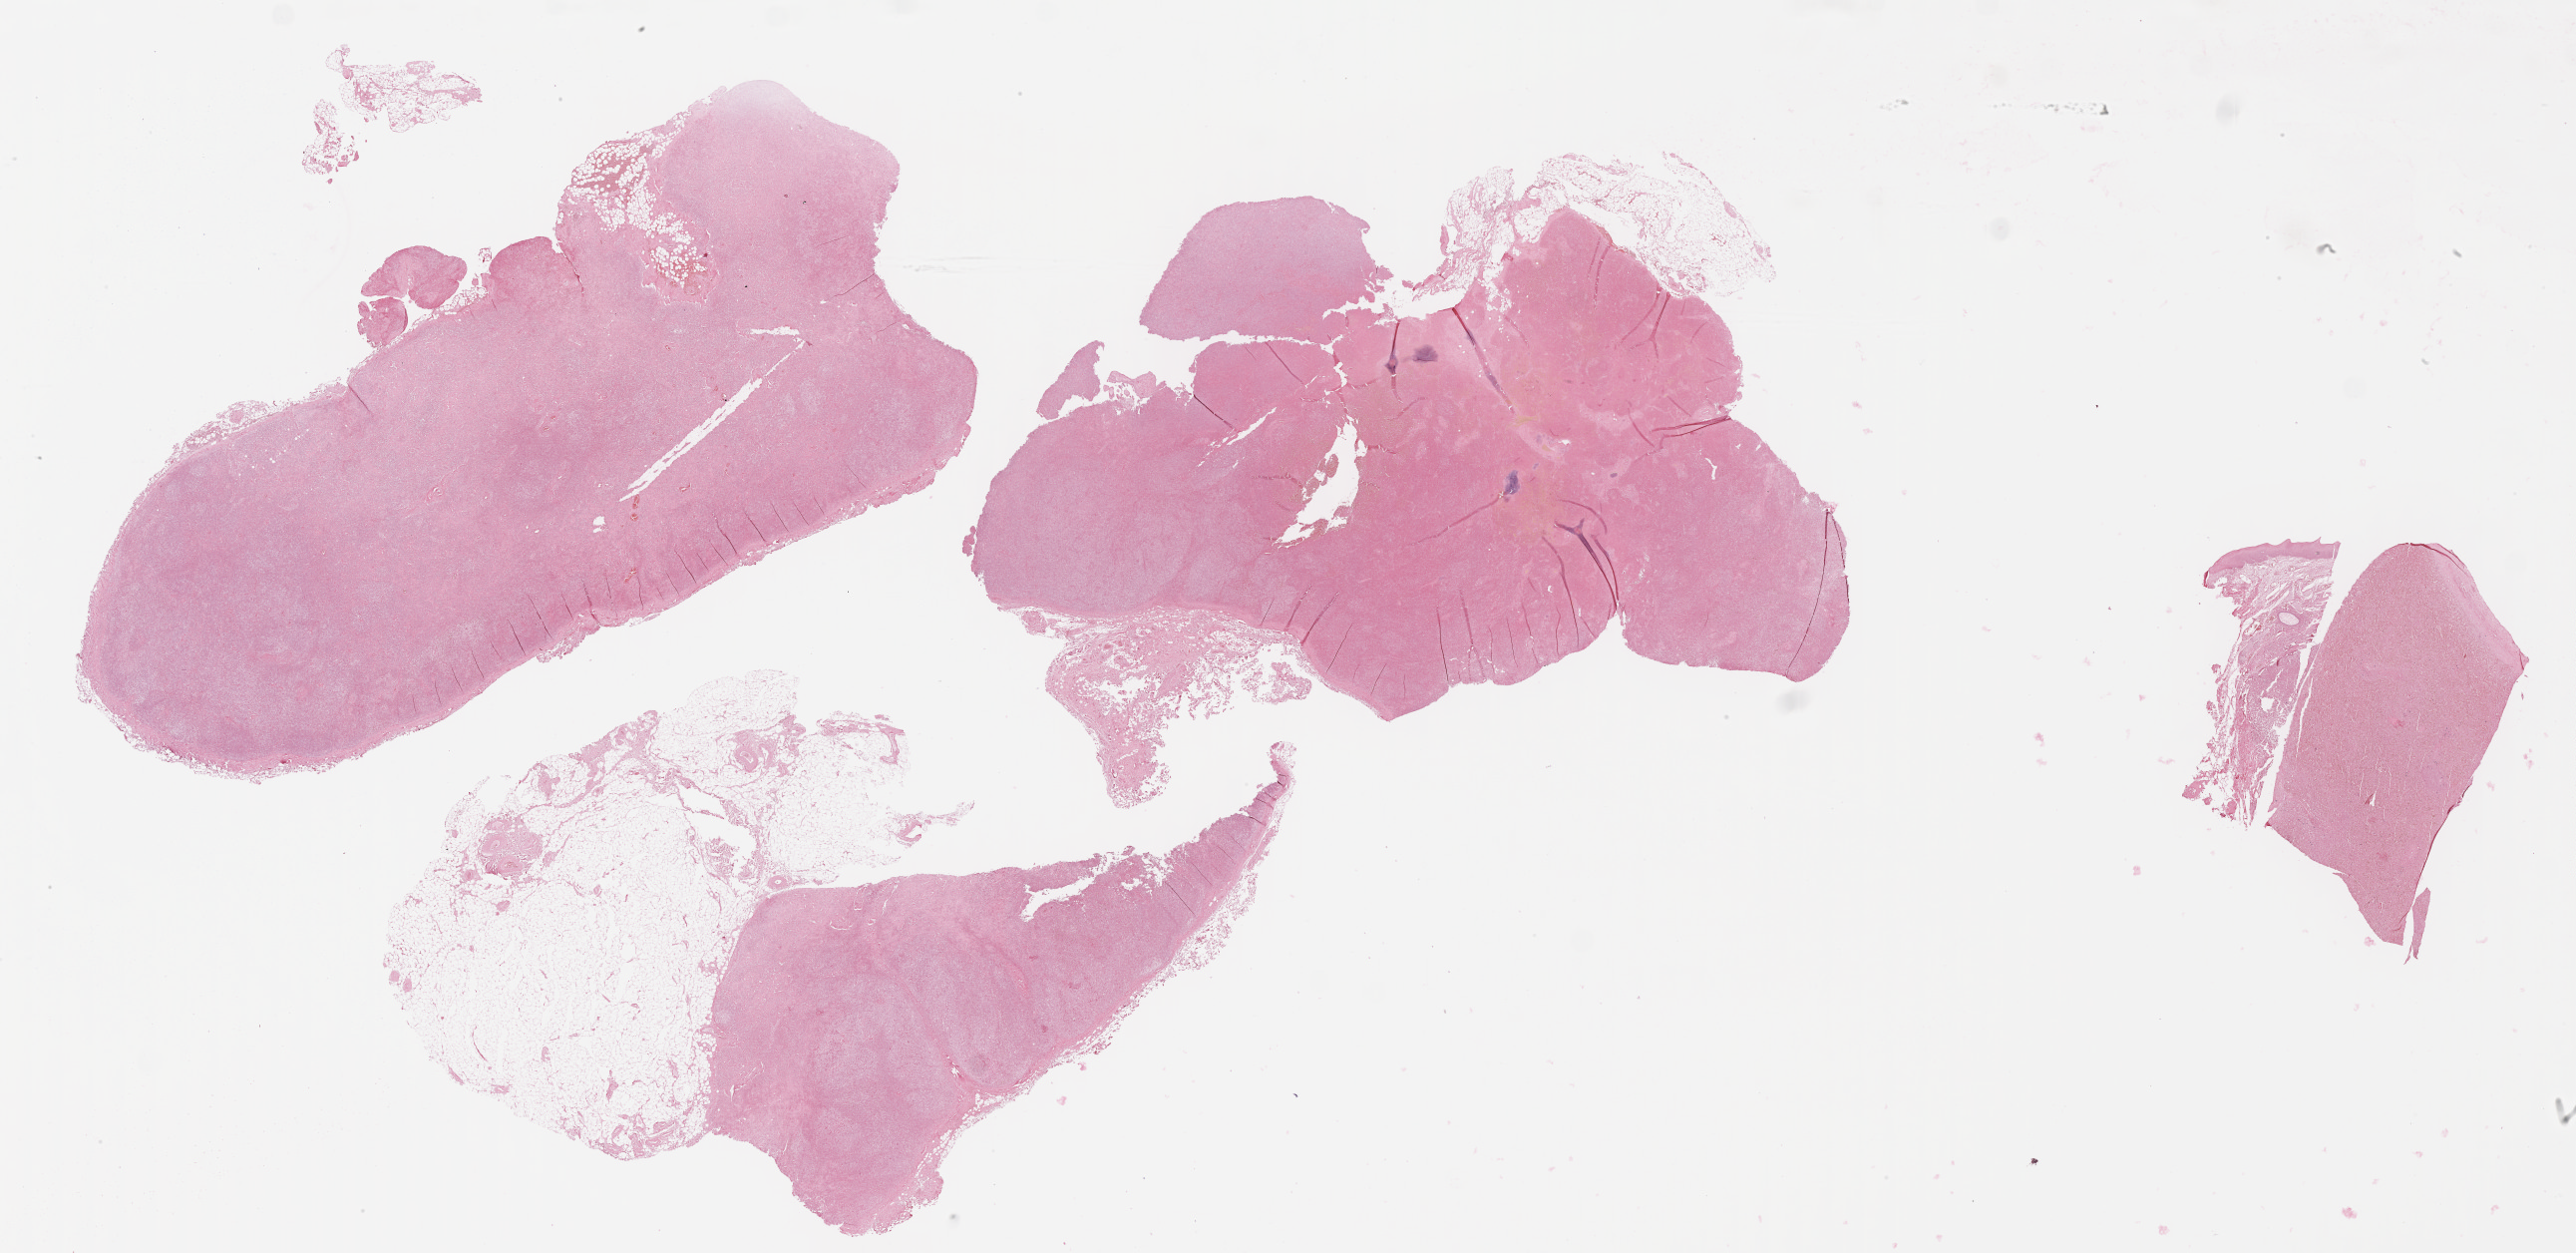
Whole-slide image, Epstein–Barr virus-encoded RNA (EBER) in-situ hybridisation, a low-resolution overview of the entire scanned area, about 41.8 x 20.3 mm, tumor tissue, site: lymph node. Patient male; 56 years old.
* diagnosis: Diffuse large B-cell lymphoma, NOS